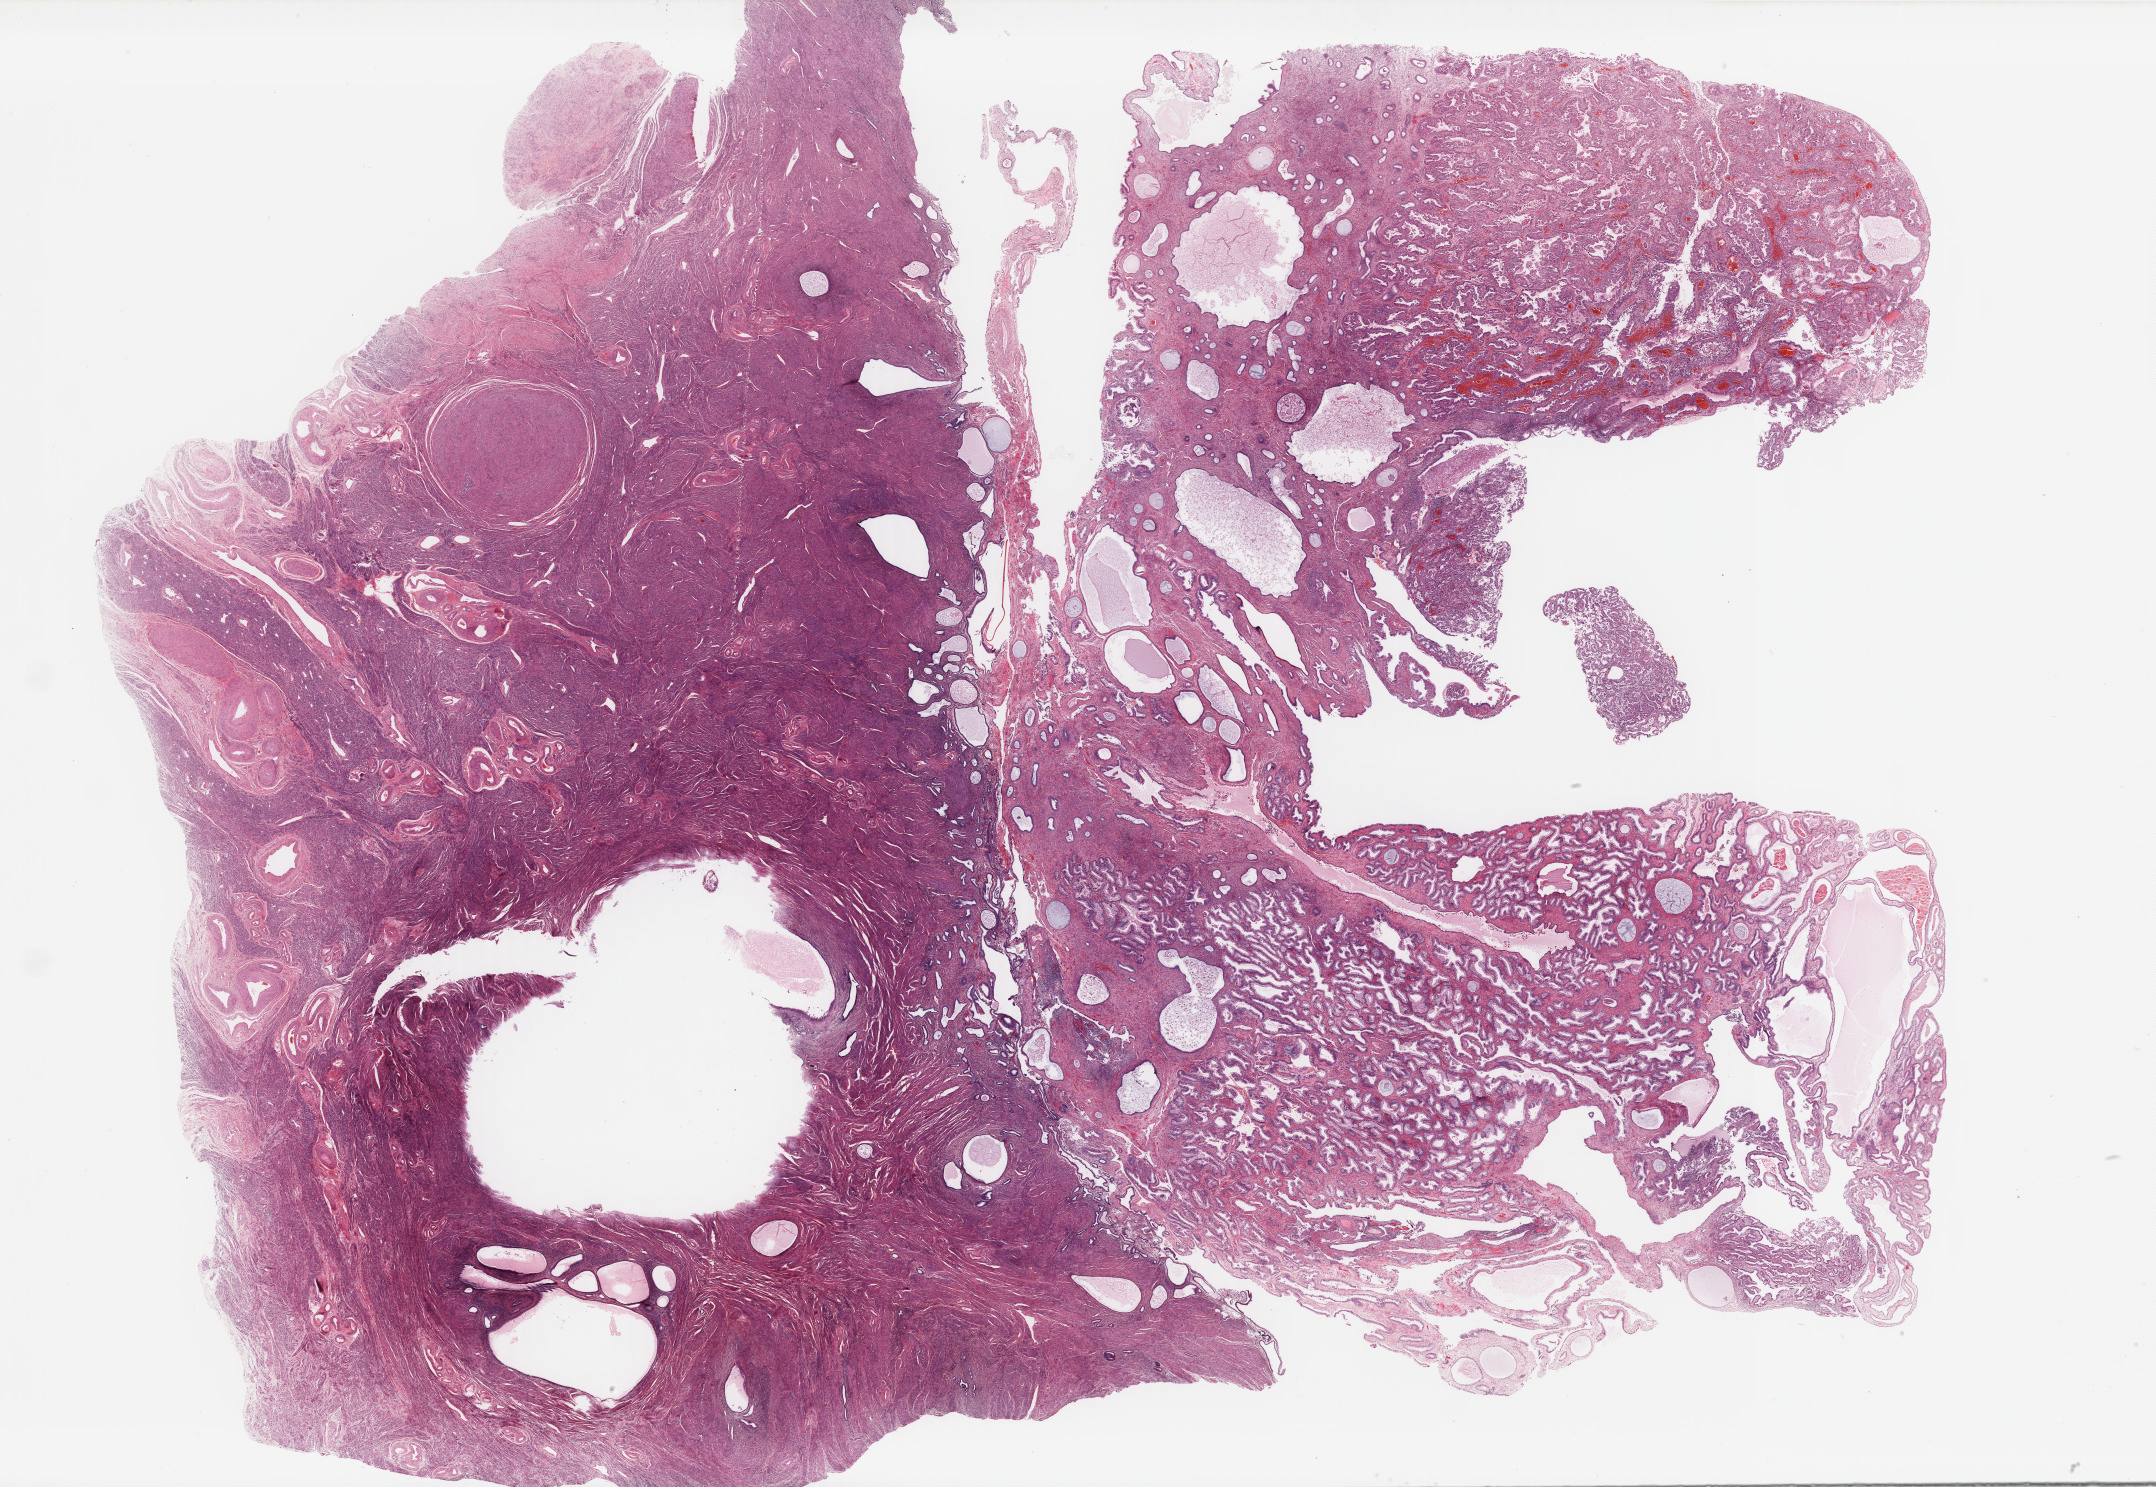
Digitized H&E-stained tissue section (whole slide), a low-resolution overview of the entire scanned area, about 34.2 x 23.6 mm, FFPE section, sample: primary tumour, uterus. Patient: female, age at initial diagnosis 69 years. Histologic grade: G2 (moderately differentiated).
• FIGO stage: IA
• histologic diagnosis: Endometrioid adenocarcinoma, NOS (endometrium)